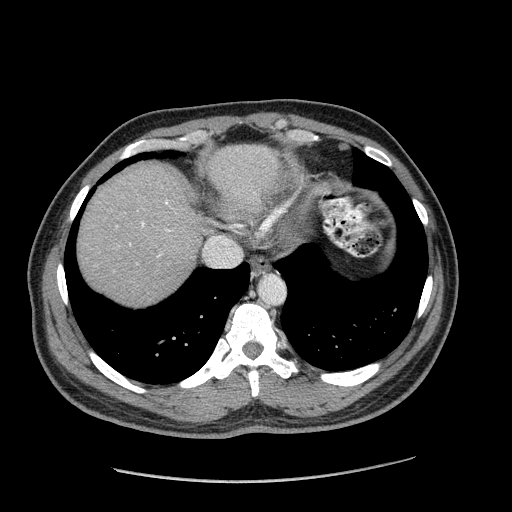
Contrast-enhanced abdominal CT (liver protocol), one axial slice; position 157 of 182 along the scan axis; reconstruction kernel STANDARD; 120 kVp; soft-tissue window (W 400 / L 40 HU); 2.5 mm slice thickness; 512 × 512 image matrix, field of view 400 × 400 mm. From the clinical record (not read from this slice): diagnosis: hepatocellular carcinoma (patient treated with transarterial chemoembolisation; whether this scan precedes or follows treatment is not stated here); TNM stage (as recorded): Stage-I; Child-Pugh class: A; tumour differentiation: well differentiated; tumour nodularity: uninodular.
Structures marked on this image (semi-automatic segmentation, software-assisted and operator-edited):
- abdominal aorta: bounding box (x1, y1, x2, y2) in pixels: (259, 275, 285, 304)
- liver parenchyma outside the tumour (the mass and vessels are separate outlines, so this box may not span the whole liver): (78, 144, 278, 304)
- liver vessels: (142, 202, 170, 257)